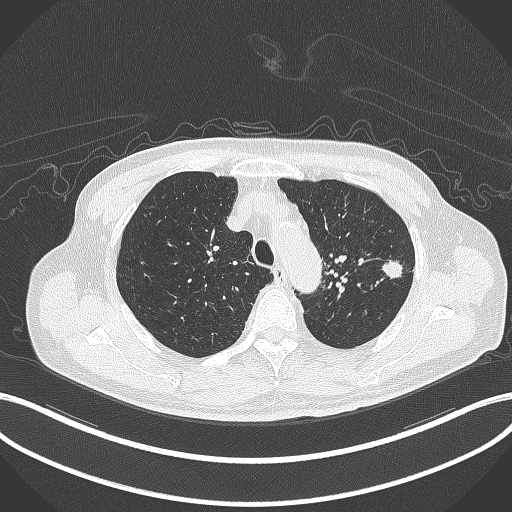
Chest CT, one axial slice. Slice 345 of 417 in the series (ordered by position). Lung window (W 1500 / L -600 HU). 1 mm slice thickness. 512 × 512 image matrix, field of view 400 × 400 mm. Patient: male, 77 years. From the clinical record (not read from this slice): clinical TNM (as recorded): T3 N1 M0.
Outlined on this slice (bounding box drawn by a radiologist):
- lung tumour (recorded histology: adenocarcinoma): bounding box [x1, y1, x2, y2] px = [382, 256, 404, 286]